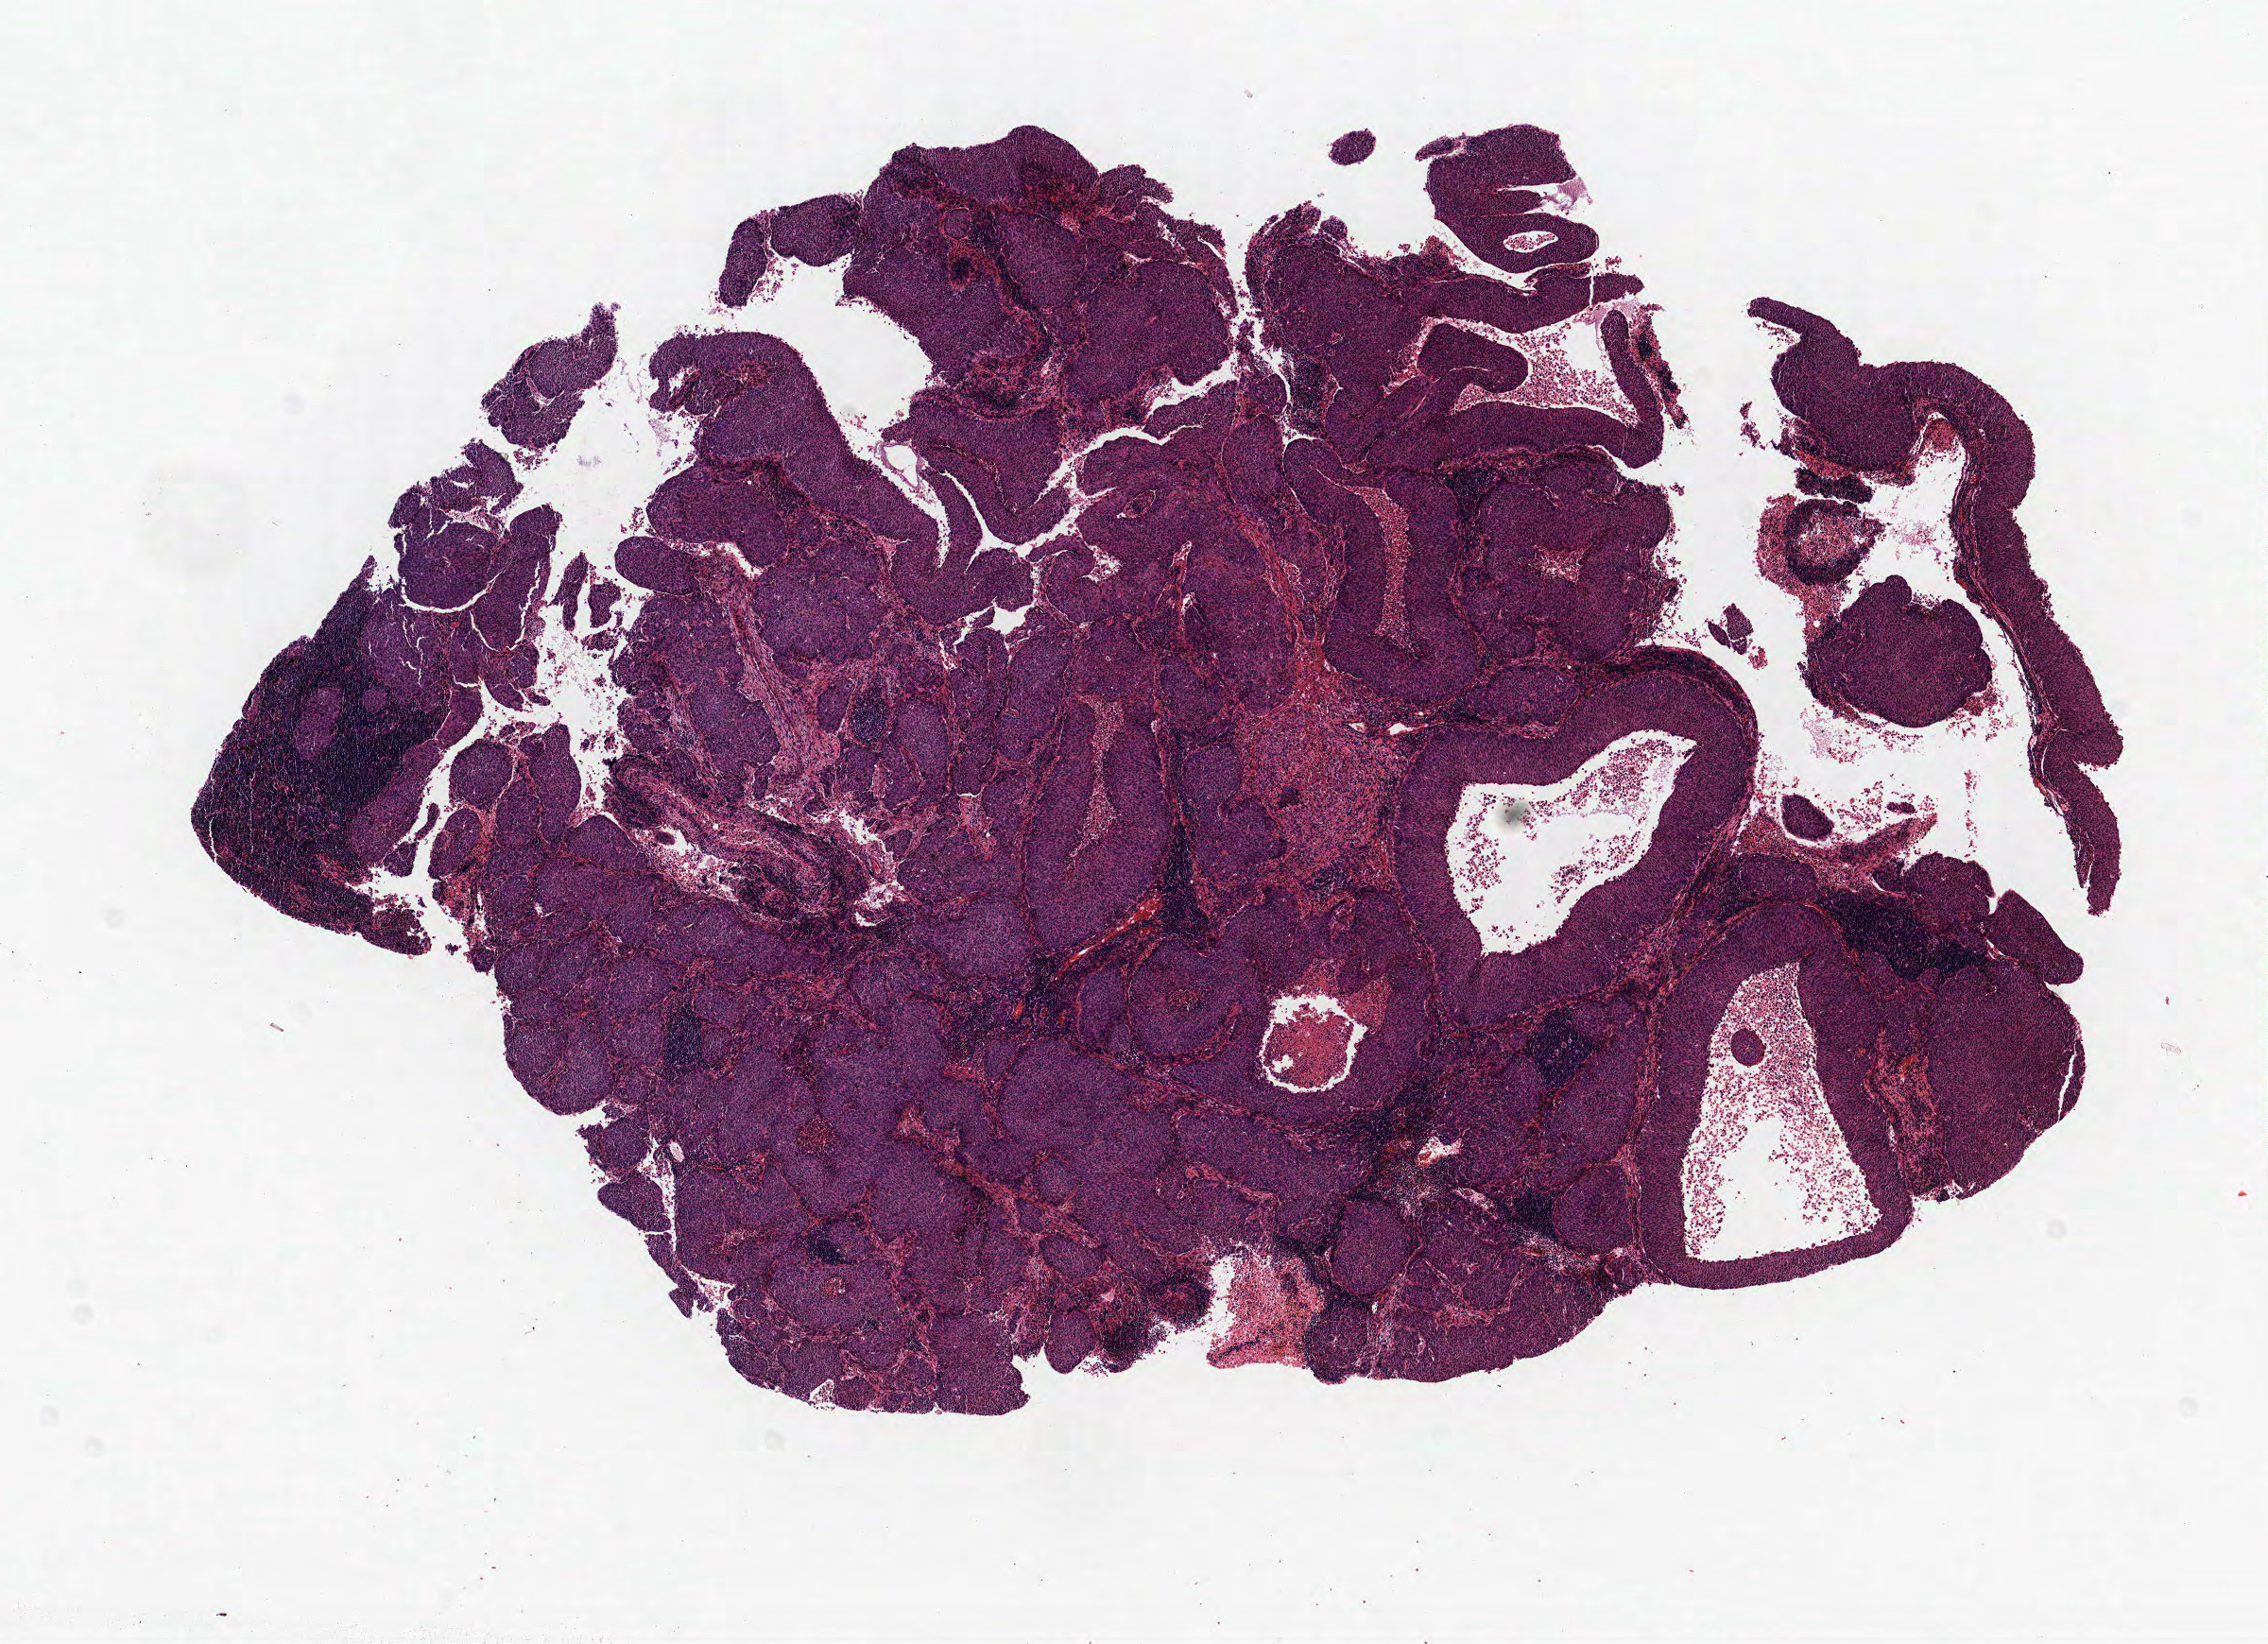
Hematoxylin and eosin (H&E) stained whole-slide image, low-resolution overview of the scanned area, about 9.6 x 7.0 mm (slide scanned at 40x). Formalin-fixed paraffin-embedded (FFPE) section. Lung tissue. Female, age 66 at enrolment.
Participant's lung-cancer diagnosis: Squamous cell carcinoma, NOS.